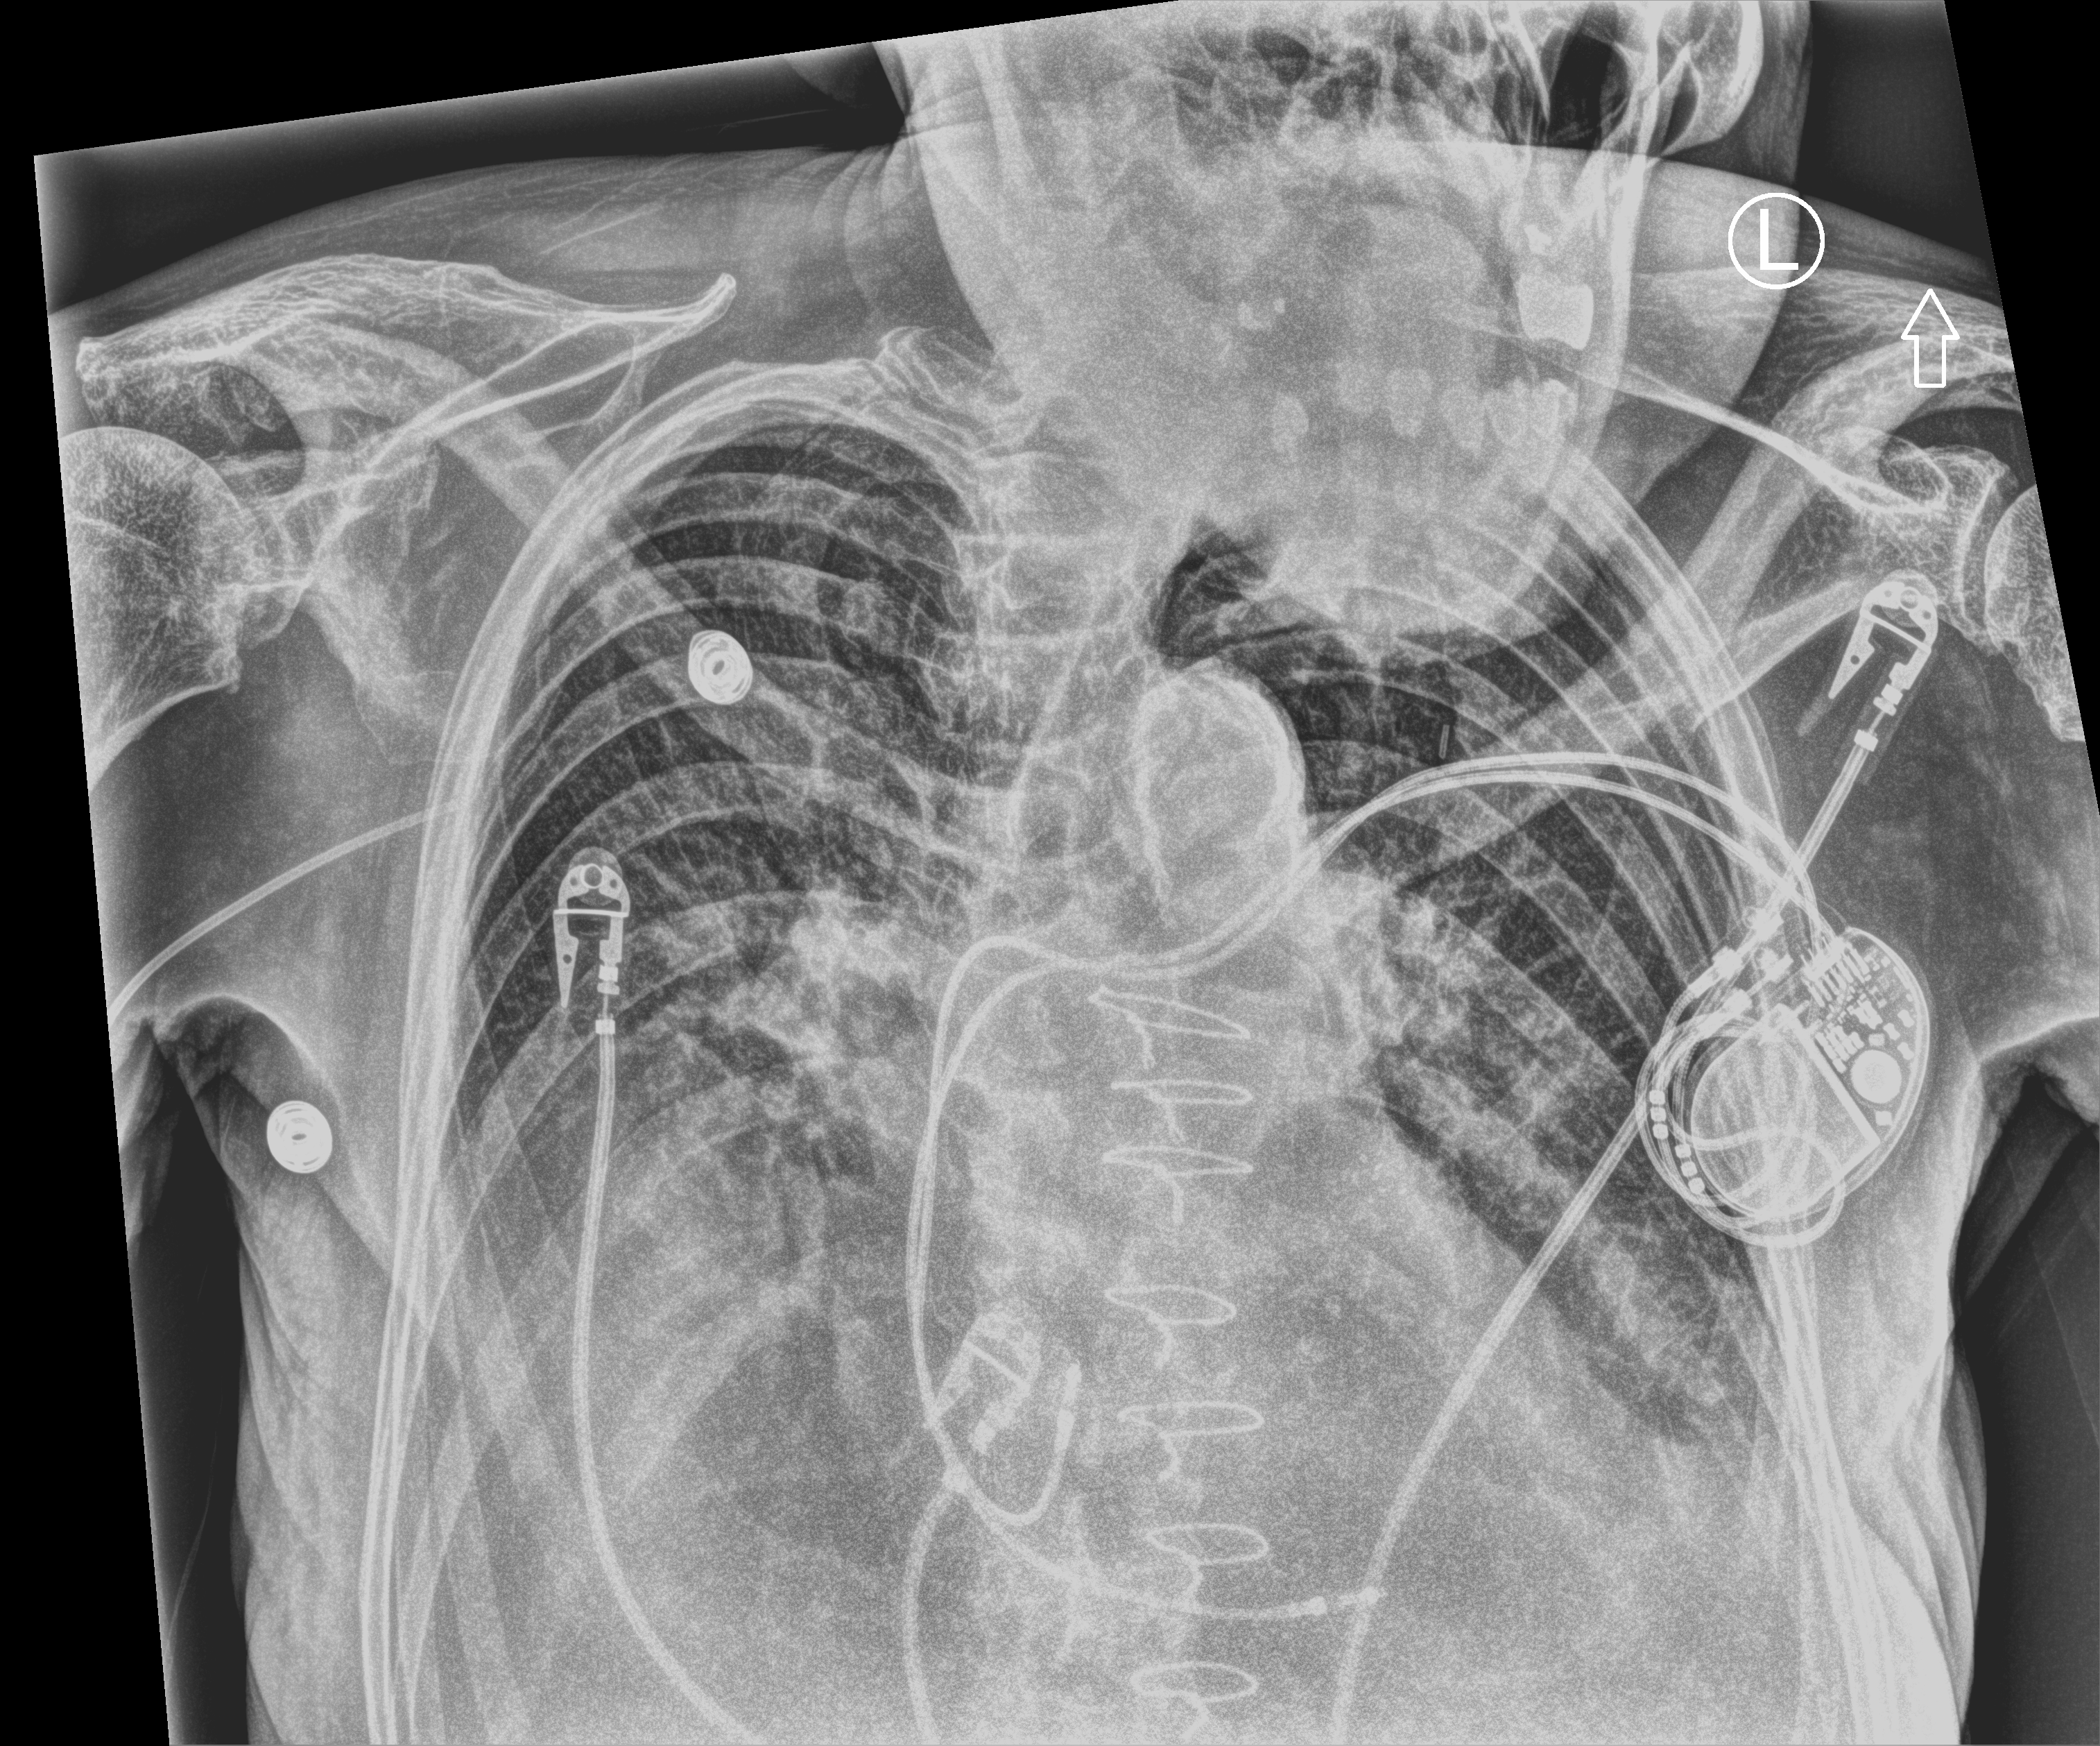
Bedside chest radiograph (computed radiography), anteroposterior (AP) projection. Male patient hospitalised with COVID-19, age 60–74 years.
Hospital-stay facts (about this admission, not read from this image; timing relative to this image not recorded): smoking status (admission record): never; mechanically ventilated during this hospital stay: no; admitted to intensive care during this hospital stay: no.